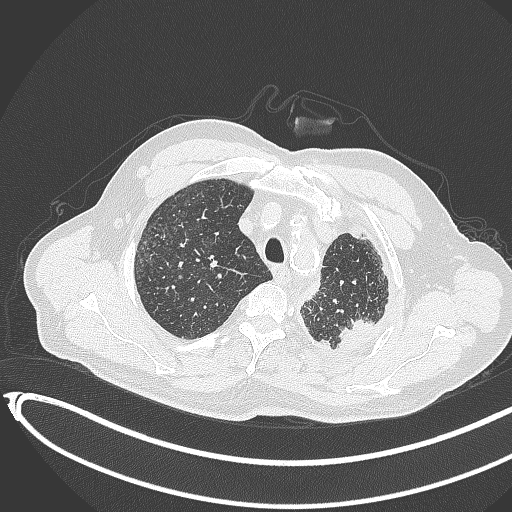
Chest CT, one axial slice; position 356 of 451 along the scan axis; reconstruction kernel B70f; 120 kVp; lung window (W 1500 / L -600 HU); 1 mm slice thickness; 512 × 512 image matrix, field of view 400 × 400 mm. Male patient, age 78 years. Case-level facts recorded for this patient, not image findings: clinical TNM (as recorded): T1c N0 M1.
Annotated regions visible in this slice (bounding box drawn by a radiologist):
- lung tumour (recorded histology: adenocarcinoma): bounding box <336,317,378,361> (left, top, right, bottom; pixels)